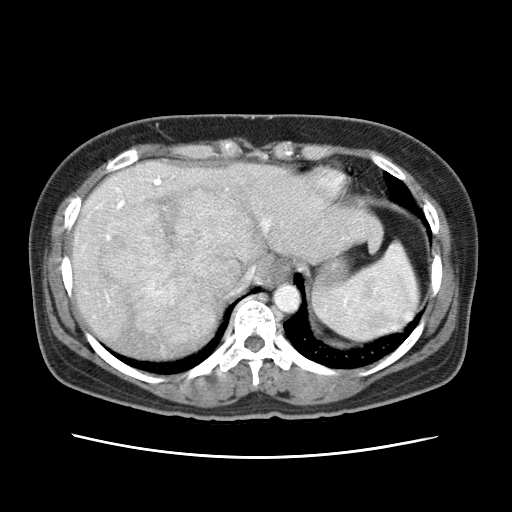
Contrast-enhanced abdominal CT (liver protocol), one axial slice. Position 55 of 79 along the scan axis. Reconstruction kernel STANDARD. Soft-tissue window (W 400 / L 40 HU). 512 × 512 image matrix, field of view 340 × 340 mm. Case-level facts recorded for this patient, not image findings: diagnosis: hepatocellular carcinoma (patient treated with transarterial chemoembolisation; whether this scan precedes or follows treatment is not stated here); TNM stage (as recorded): Stage-I; Child-Pugh class: A; tumour differentiation: moderately differentiated; tumour nodularity: uninodular.
Structures marked on this image (semi-automatically segmented with operator editing):
- abdominal aorta: bounding box (x1, y1, x2, y2) in pixels: (273, 284, 300, 314)
- liver parenchyma outside the tumour (the mass and vessels are separate outlines, so this box may not span the whole liver): (70, 160, 378, 358)
- mass: (100, 181, 263, 346)
- liver vessels: (100, 177, 269, 301)